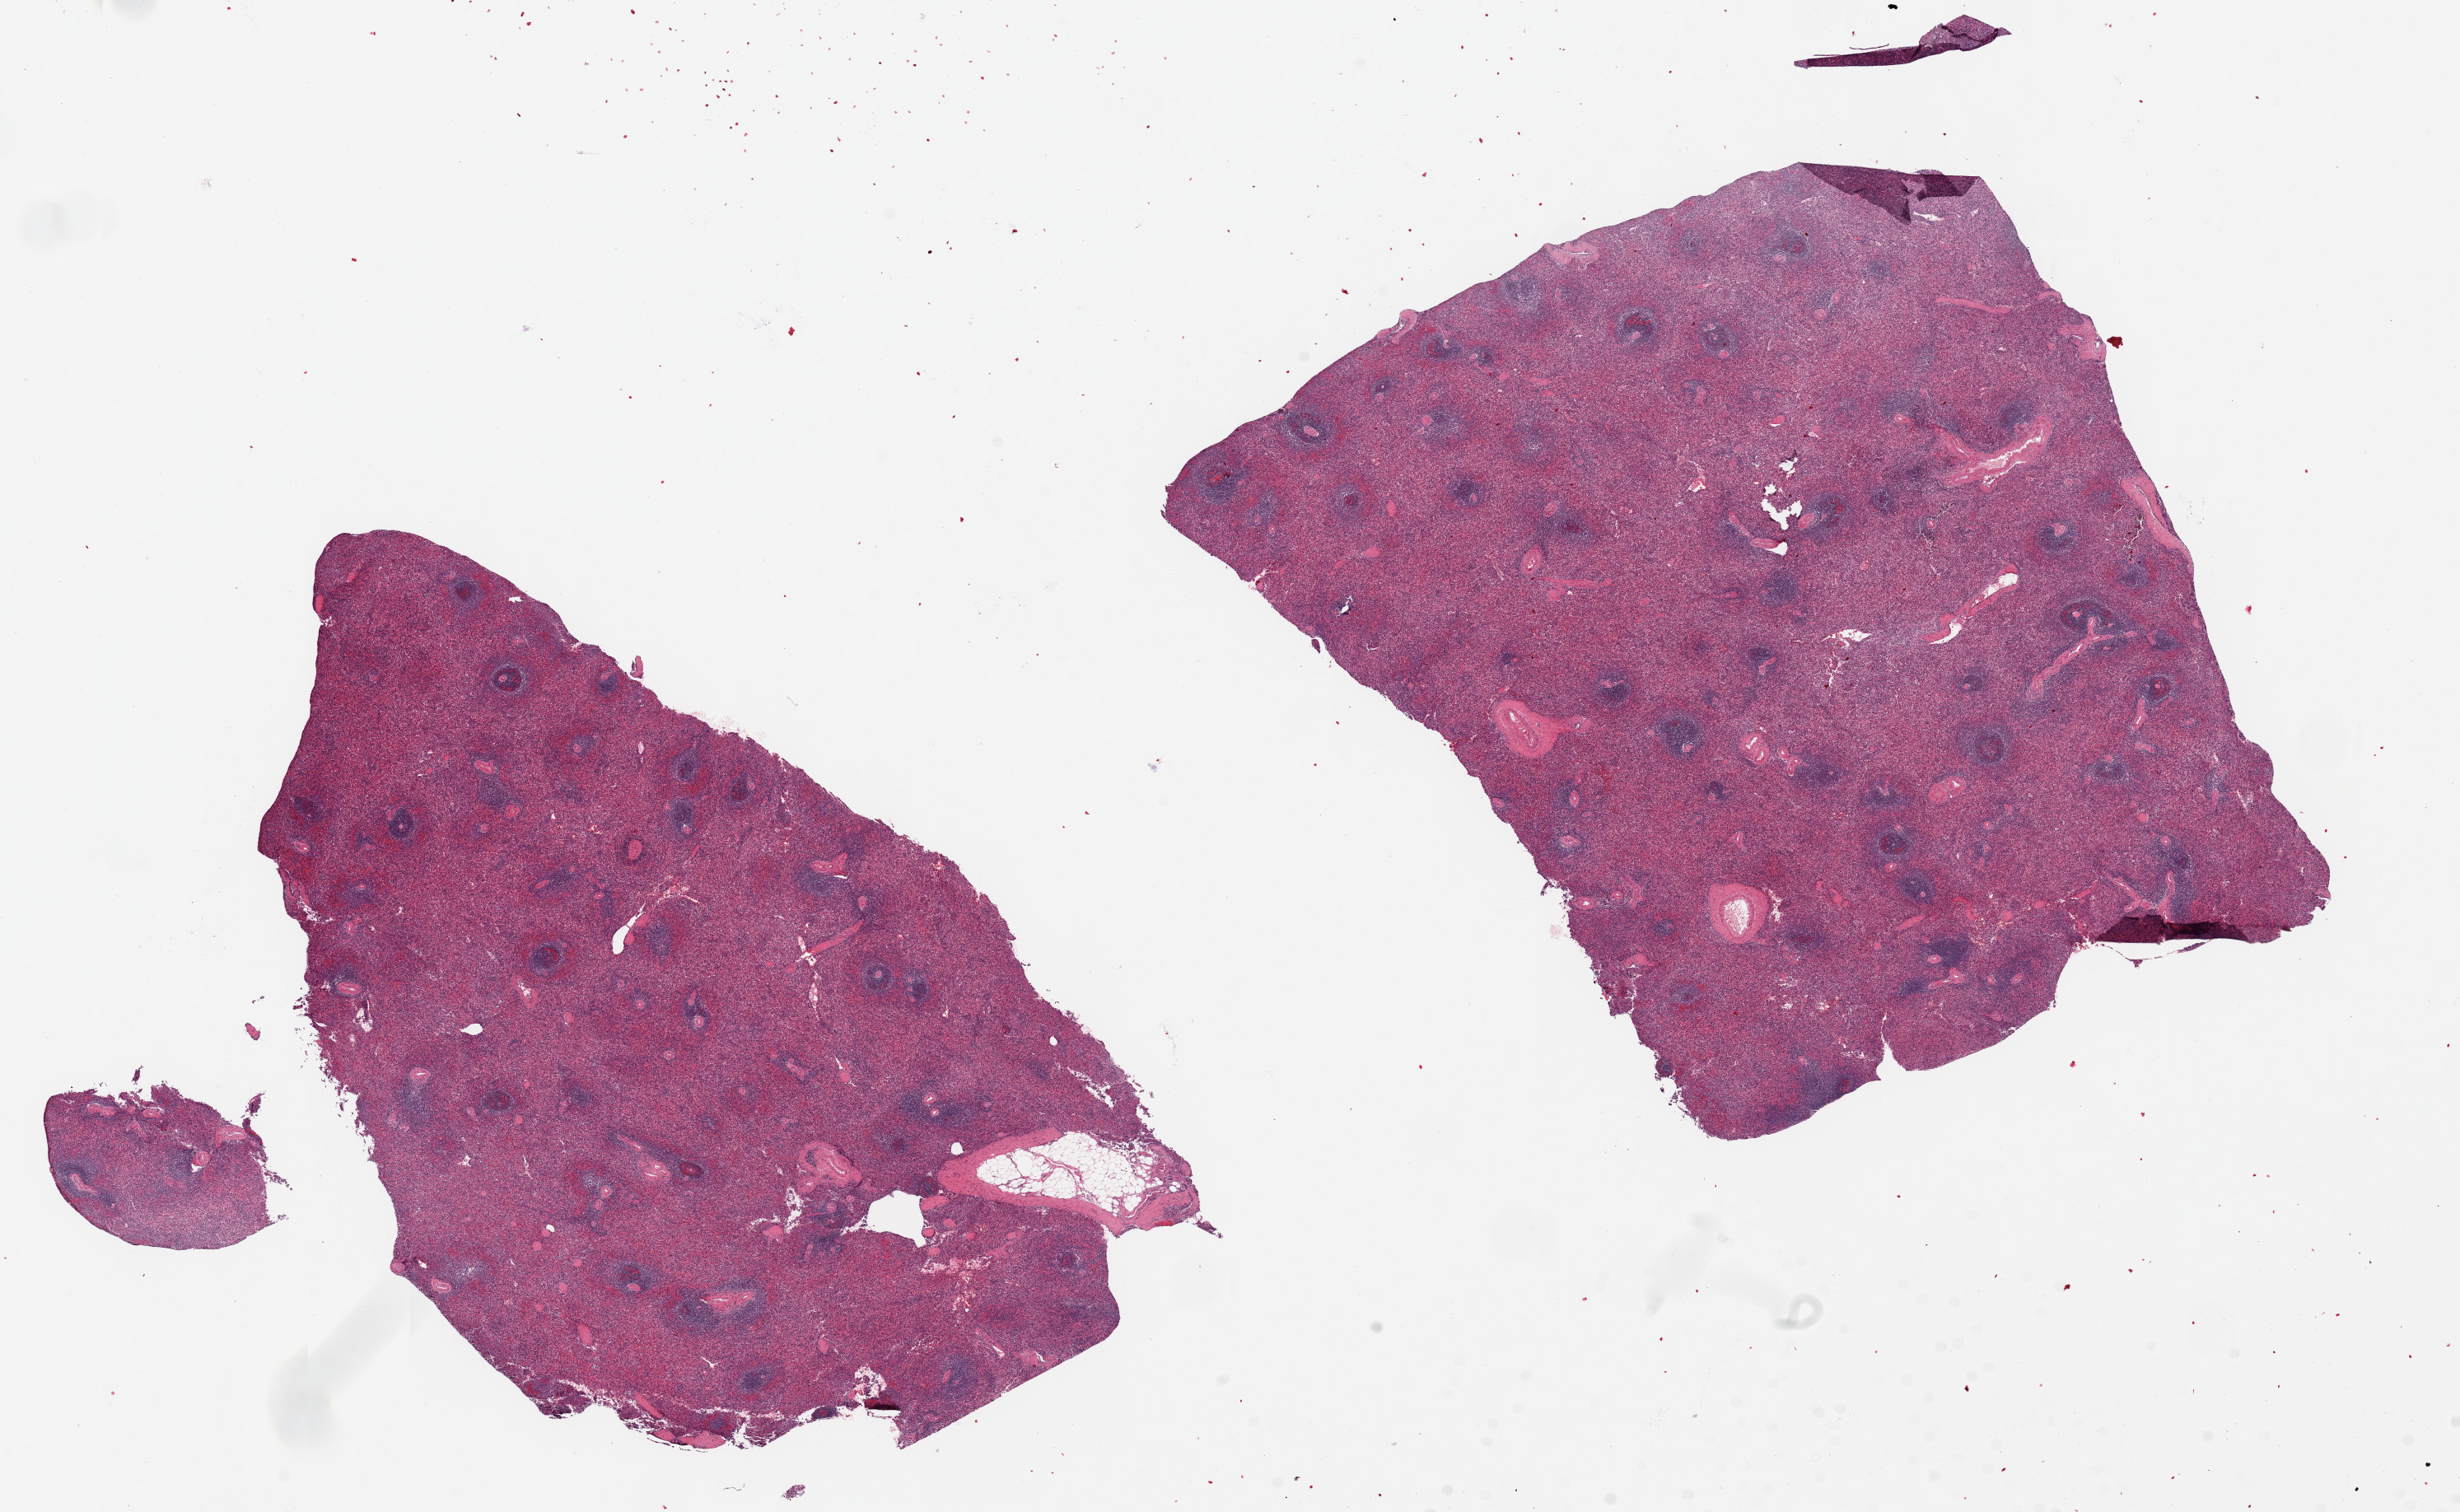
Whole-slide image, hematoxylin and eosin (H&E) stain, brightfield — low-resolution overview of the scanned area, about 23.6 x 14.5 mm (slide scanned at 20x), PAXgene-fixed paraffin-embedded (PFPE) section, section of spleen (target tissue), donor tissue sample.
Reviewer comment on this tissue sample: 2 pieces, 11x7 & 9x9mm; mild congestion.